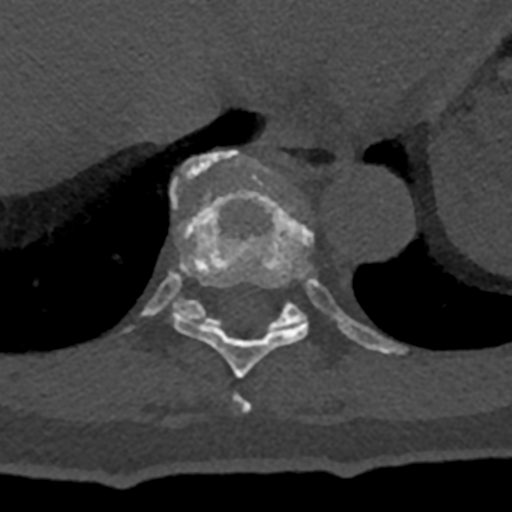
CT including the spine, one axial slice. Position 638 of 797 along the scan axis. Reconstruction kernel Br40s/3. 120 kVp. Bone window (W 1800 / L 400 HU). 512 × 512 image matrix. Patient: male, 74 years. Case-level facts recorded for this patient, not image findings: primary cancer: renal; vertebrae with lytic lesions (as recorded): T10, L1, L2, L3, L4, L5.
Outlined on this slice (semi-automatically segmented with operator editing):
- T10 vertebra: bounding box <121,150,407,355> (left, top, right, bottom; pixels)
- T8 vertebra: <234,394,251,412>
- T9 vertebra: <171,194,313,379>